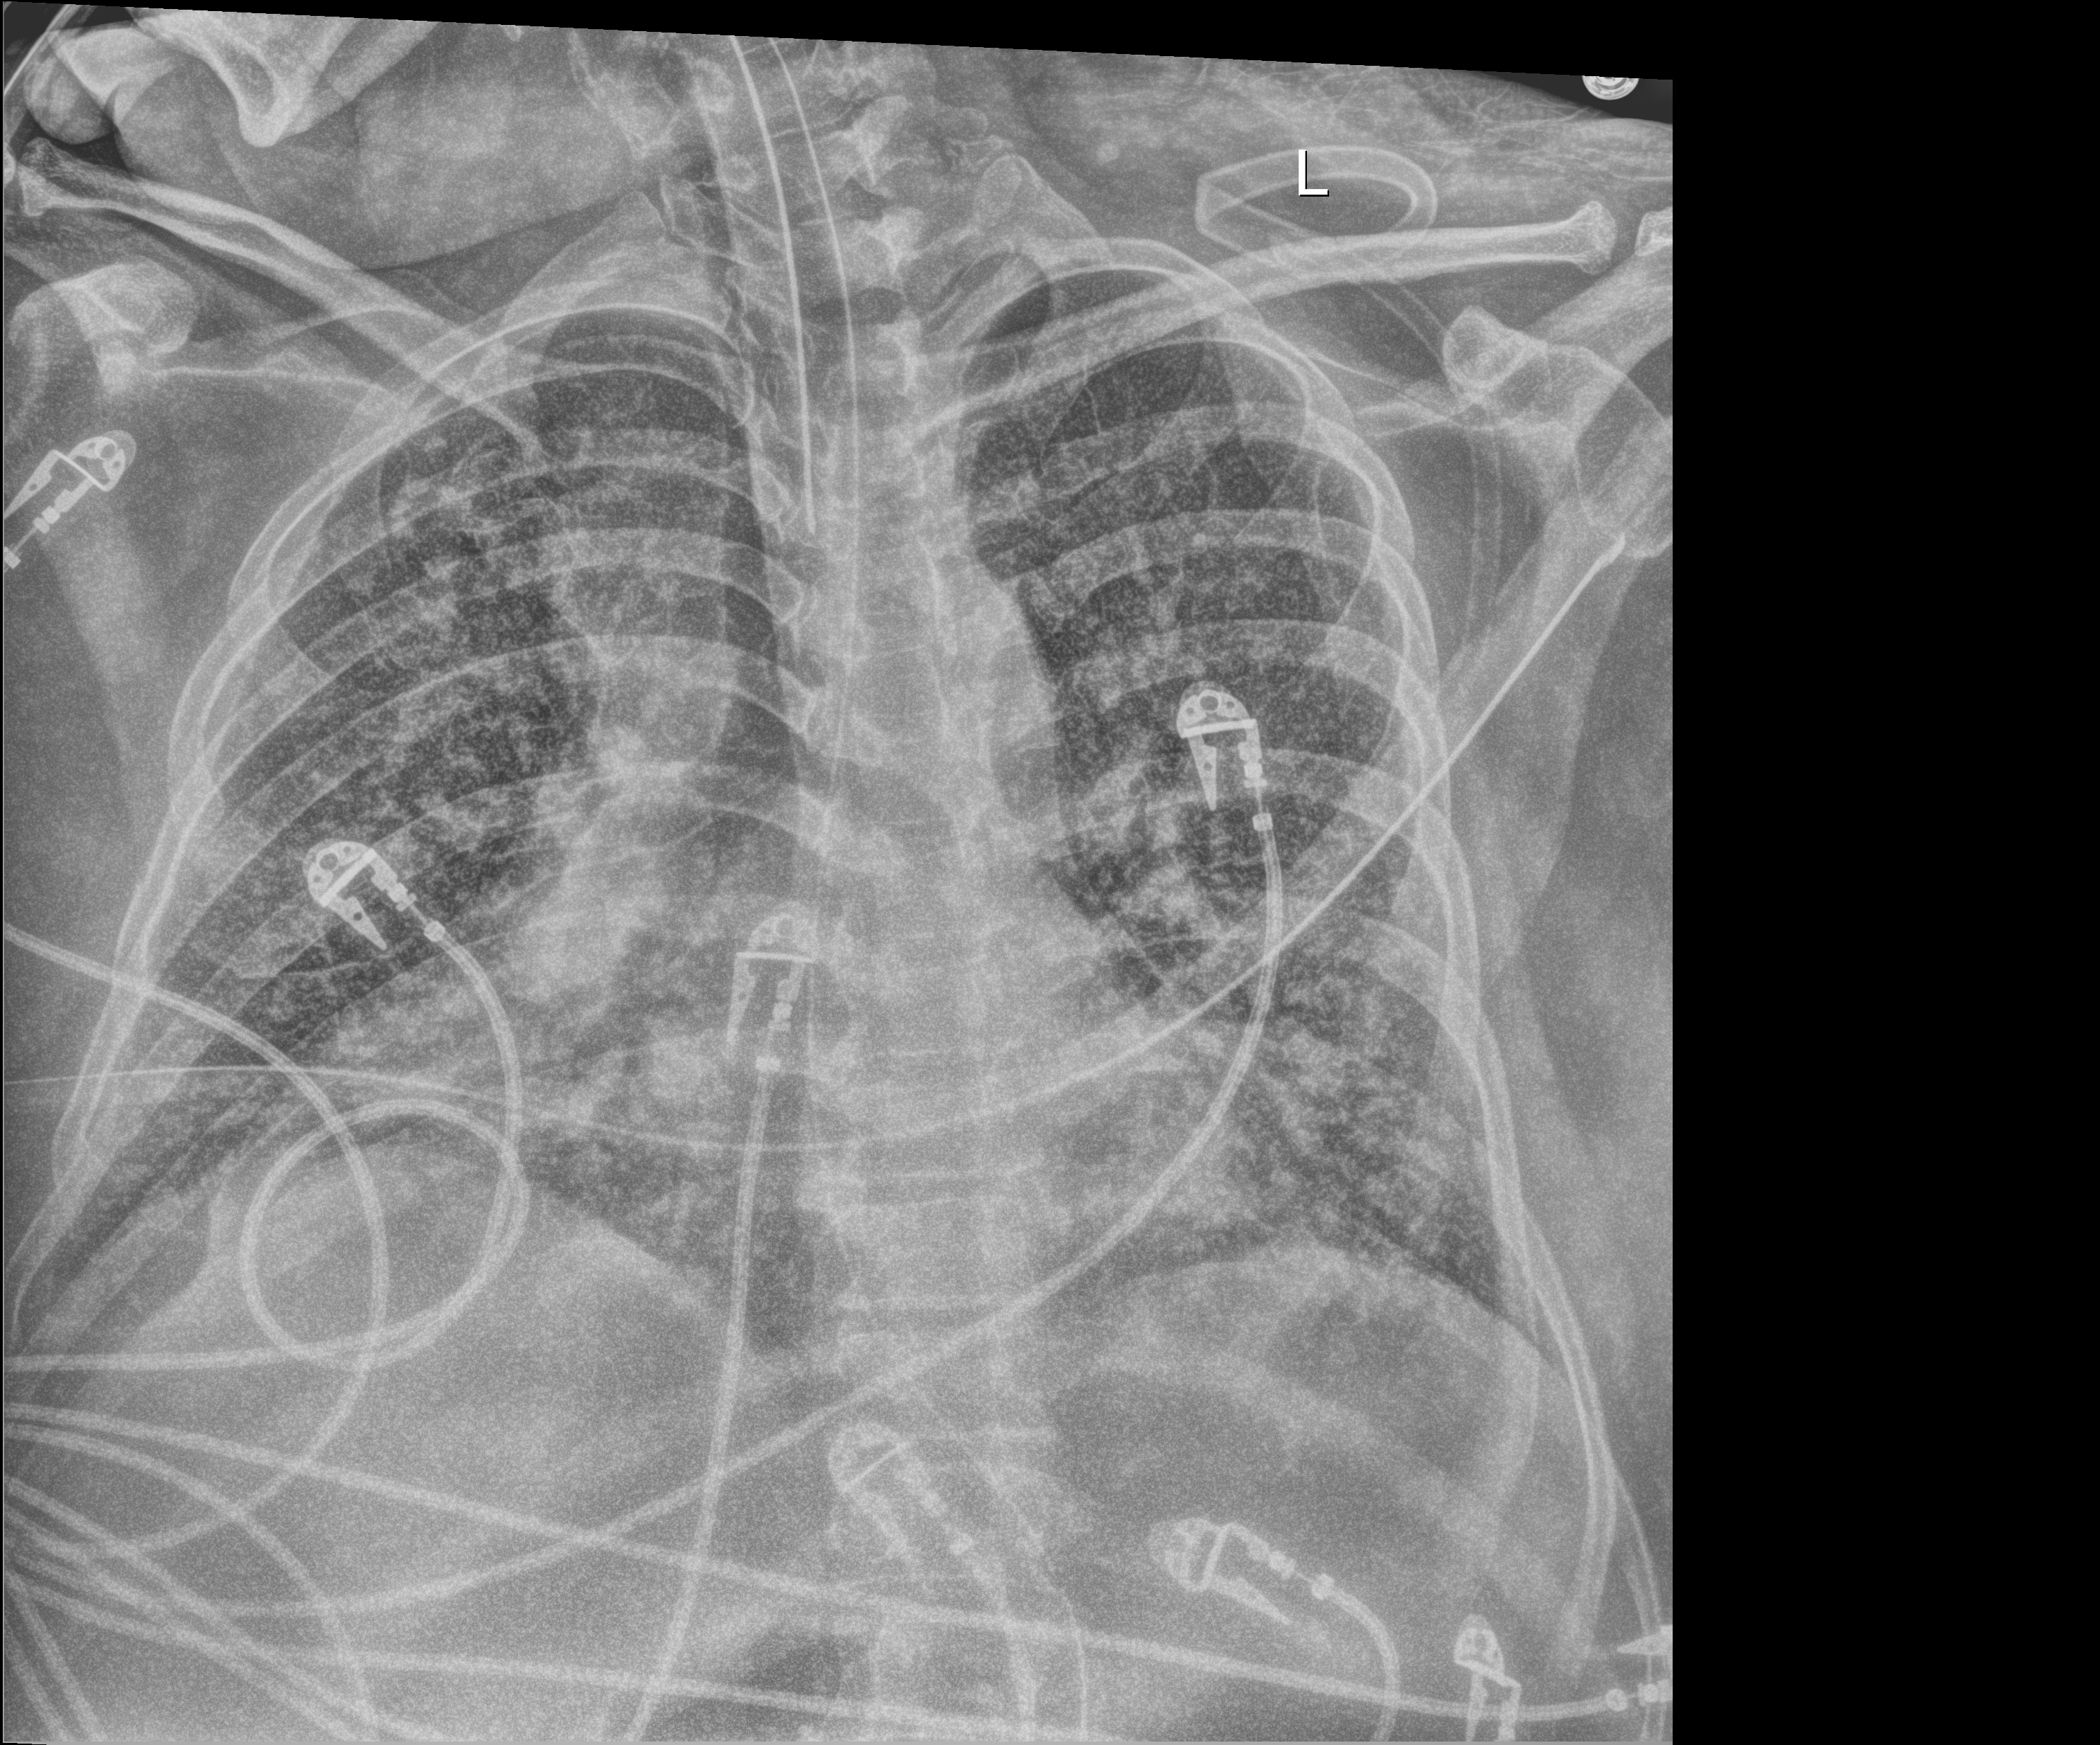
Chest X-ray (portable); anteroposterior (AP) projection. Adult patient hospitalised with COVID-19, age 18–59 years.
From the hospital-stay record, not from the radiograph (when in the stay this image was taken is not recorded):
- length of hospital stay: 48 days